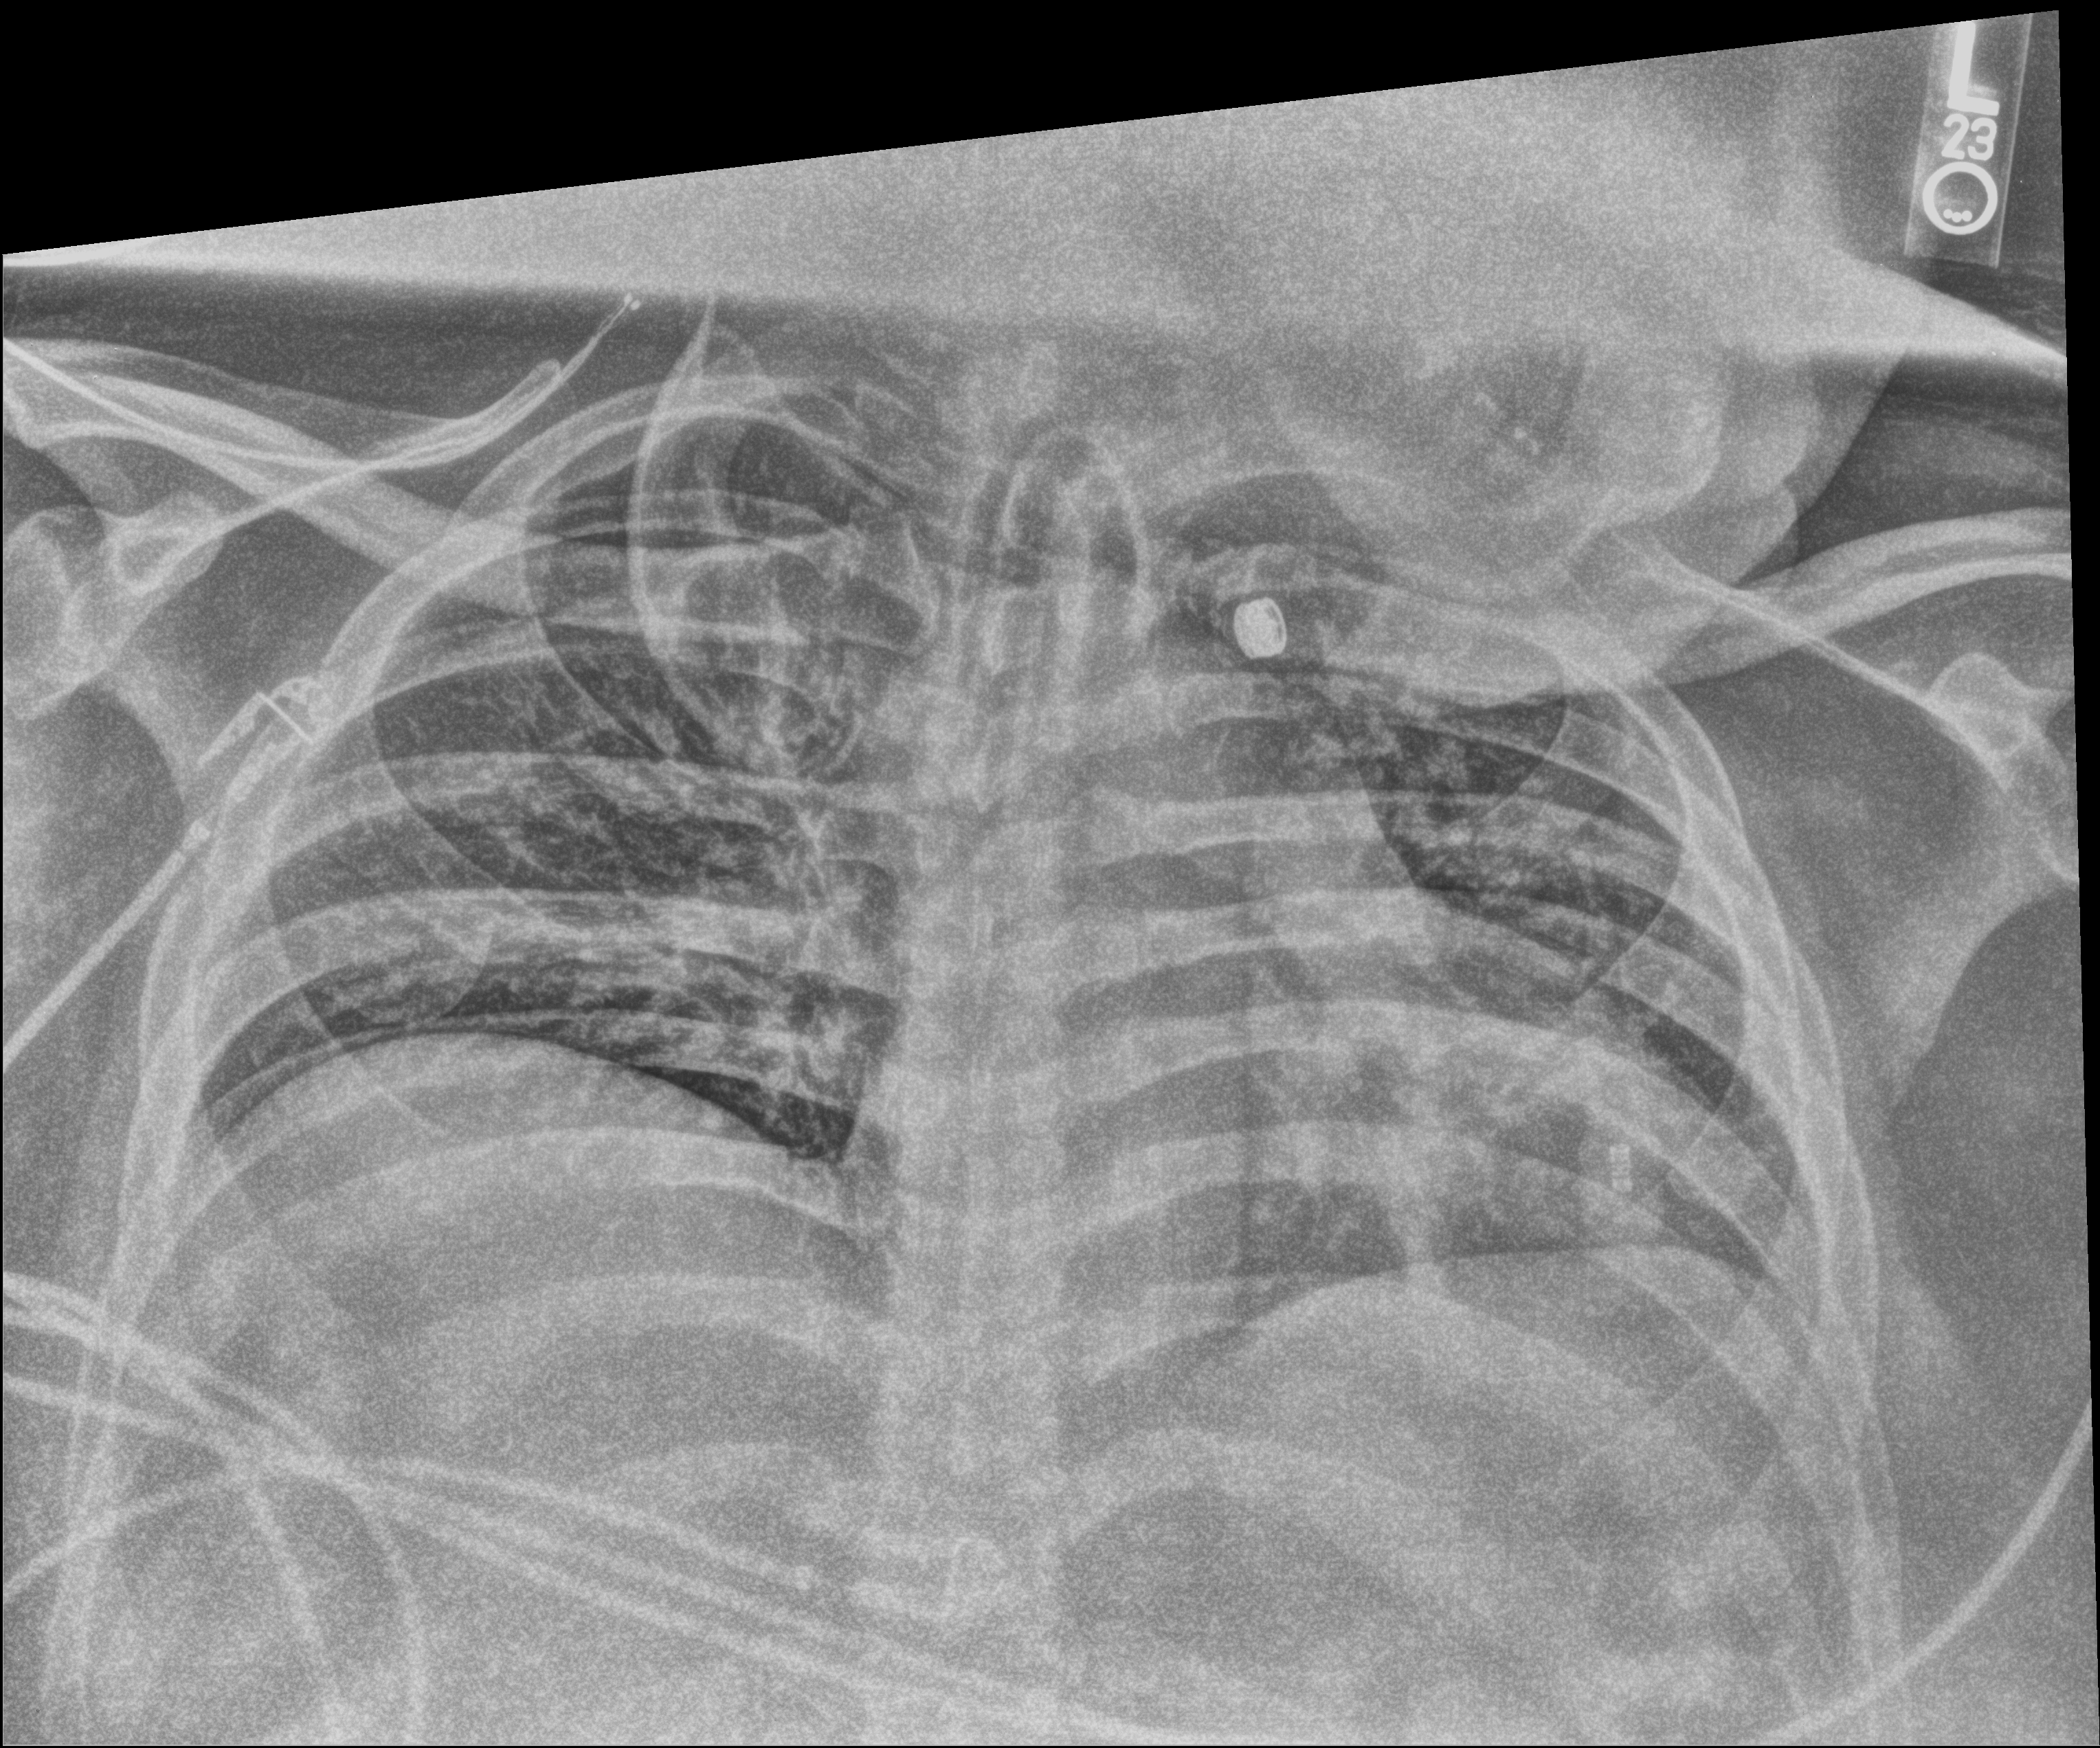
Bedside chest radiograph (computed radiography), anteroposterior (AP) projection. Patient hospitalised with COVID-19; male, aged 18–59 years.
Hospital-stay facts (about this admission, not read from this image; timing relative to this image not recorded): mechanically ventilated during this hospital stay: yes; admitted to intensive care during this hospital stay: yes; hypertension (admission record): no.